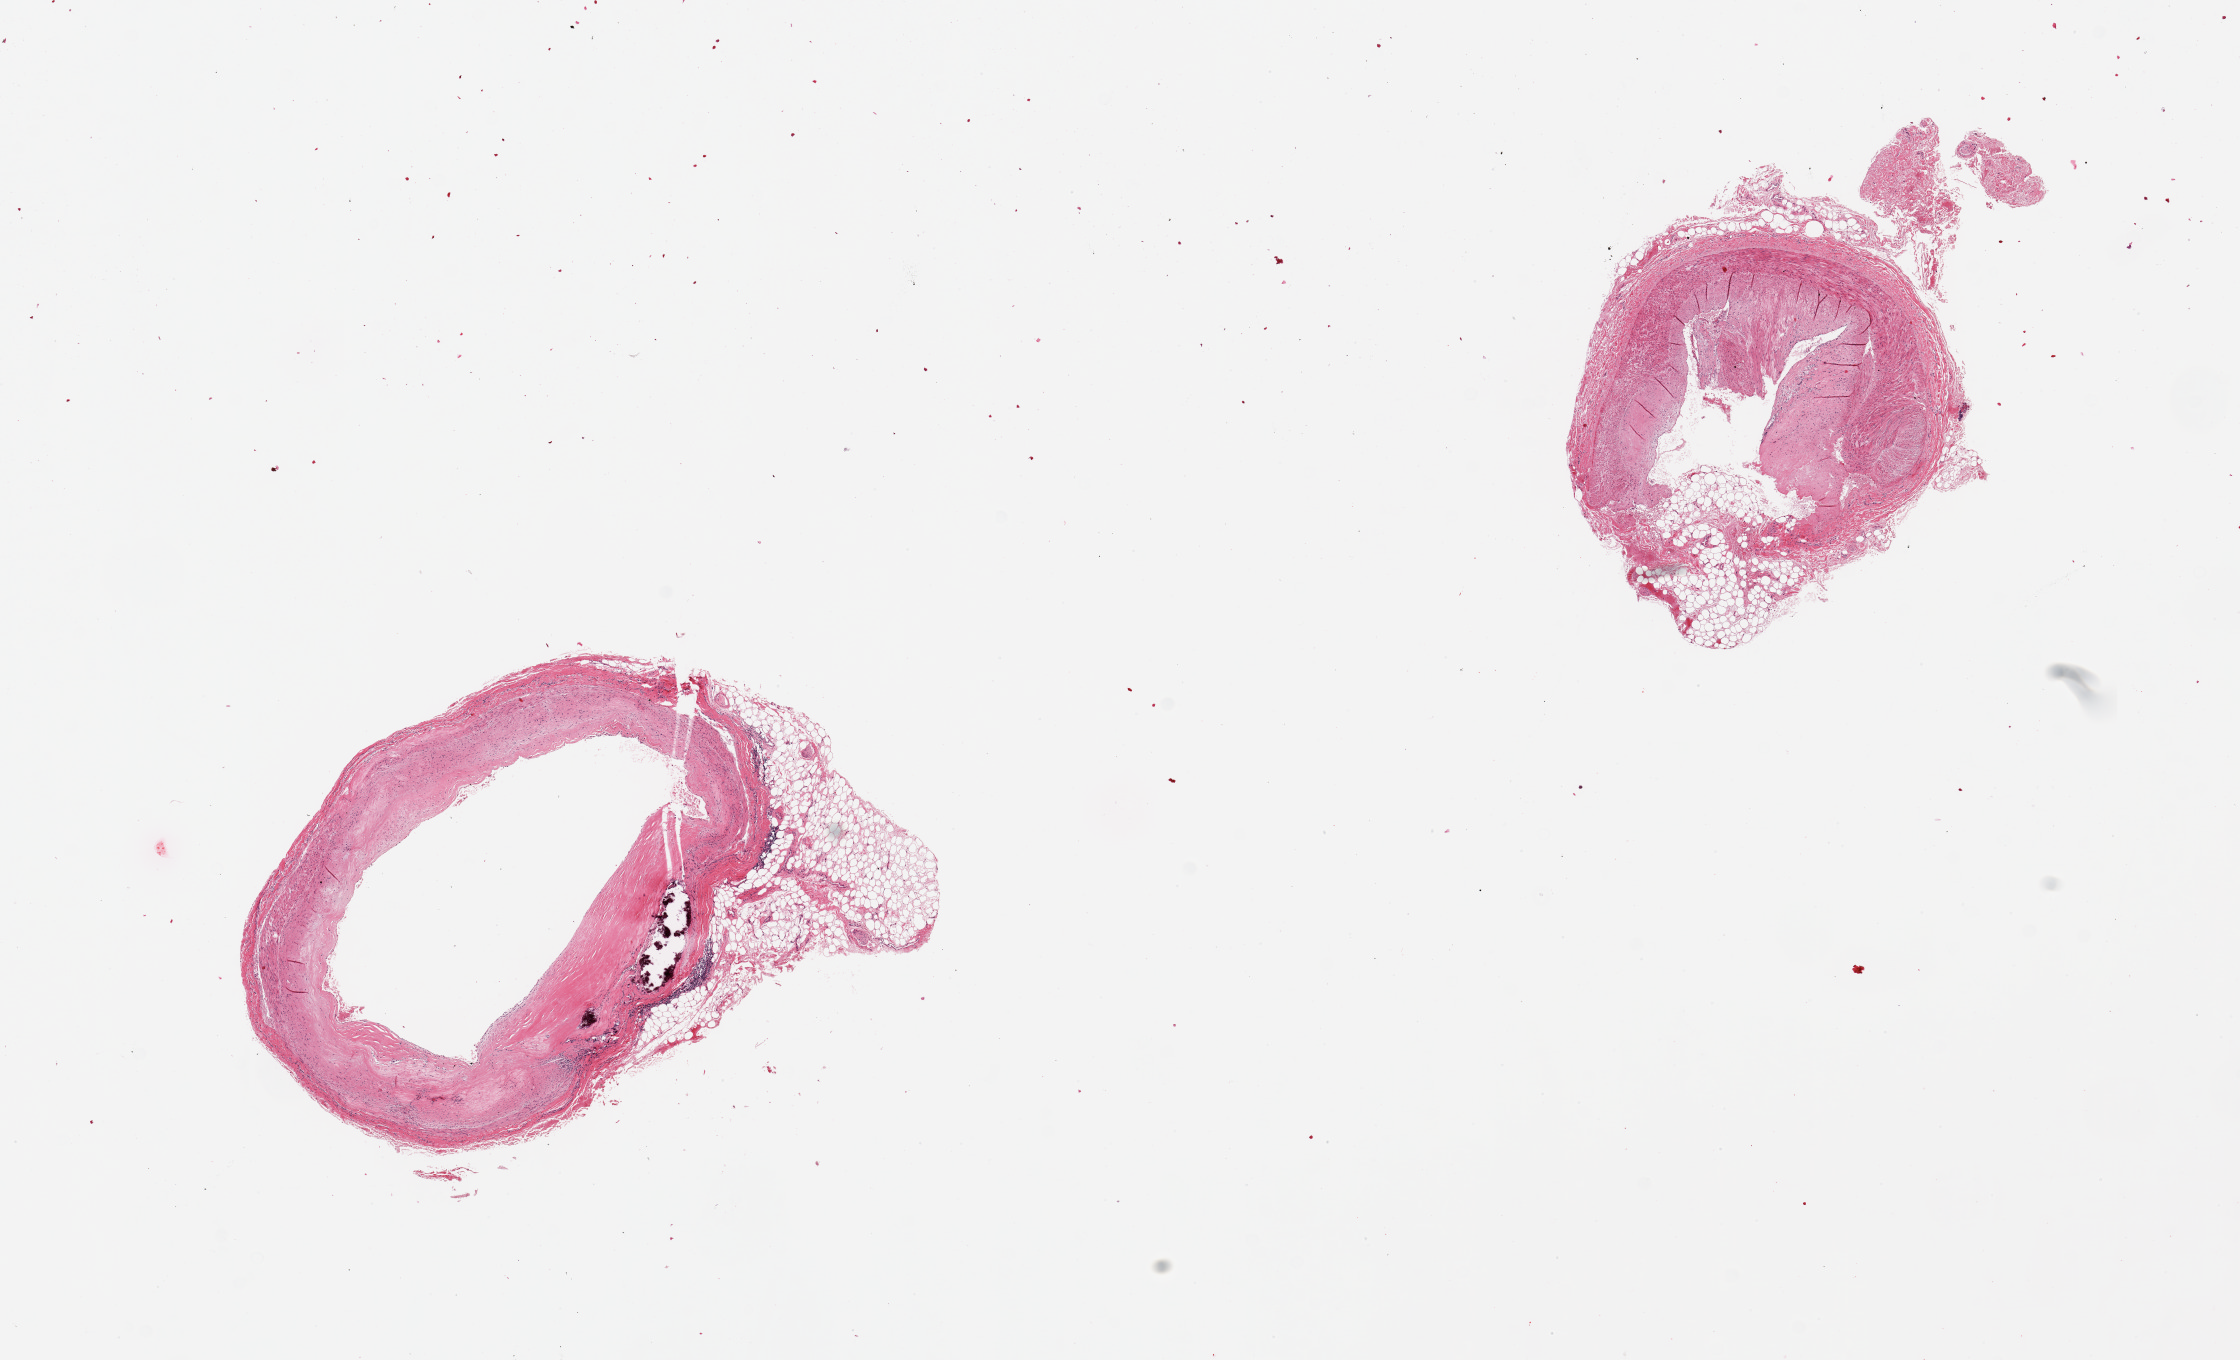
Whole-slide image, hematoxylin and eosin (H&E) stain, brightfield, low-resolution overview of the scanned area, about 17.7 x 10.8 mm (slide scanned at 20x). PAXgene-fixed paraffin-embedded (PFPE) section. Target tissue: coronary artery. Donor tissue sample.
Review note (as recorded): 2 pieces, calcific atherosclerosis, focal adventitial lymphoid deposits, perivascular fat up to 1.4mm thick.